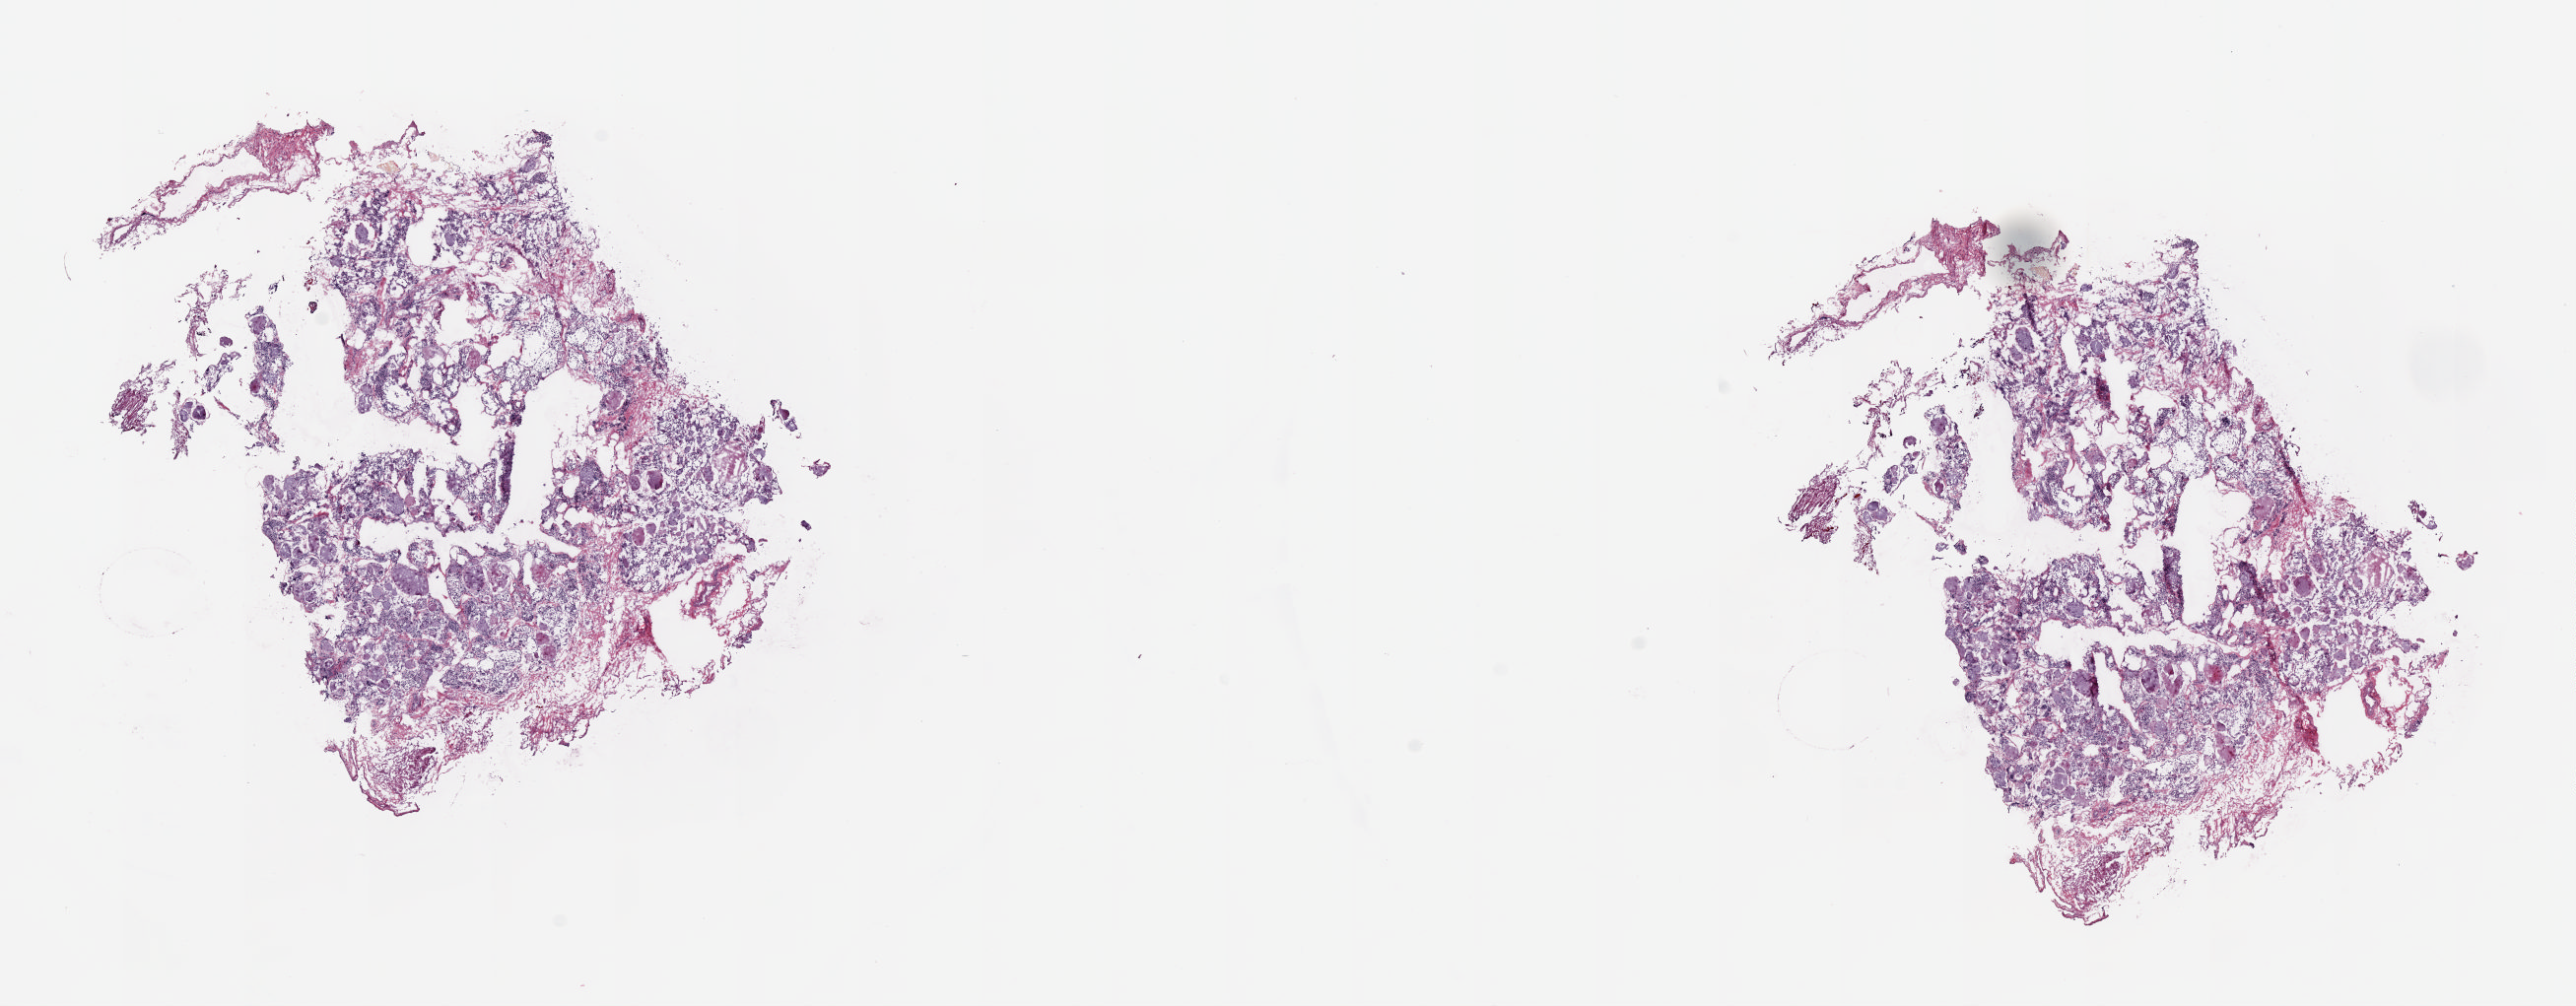
Whole-slide histology image, Hematoxylin and eosin (H&E) stained, shown as a low-resolution overview of the whole scanned area (about 20.7 x 8.1 mm, slide scanned at 20x), frozen section from the top of the tissue portion, solid tissue normal (non-tumour tissue) sample from the thyroid. Patient: female, age at initial diagnosis 69 years. Slide review estimates, as recorded: tumour cells 0%, tumour nuclei 0%, normal cells 100%, stromal cells 0%, necrosis 0%. Infiltration values recorded for this section: lymphocyte infiltration 0%, monocyte infiltration 0%, neutrophil infiltration 0%.
* this section: solid tissue normal (non-tumour) sample from the same patient
* patient diagnosis: Papillary adenocarcinoma, NOS